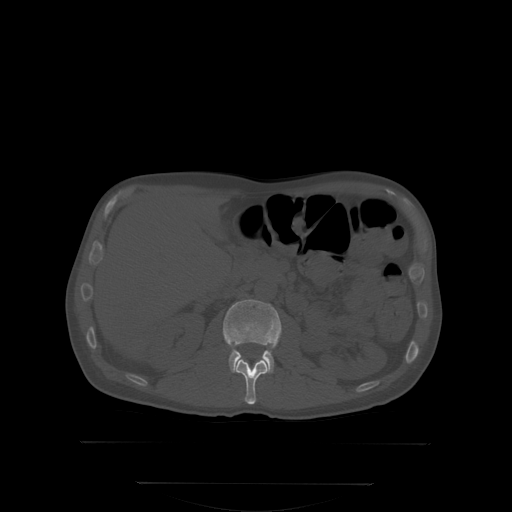
CT including the spine, one axial slice; position 145 of 350 along the scan axis; bone window (W 1800 / L 400 HU); 2.5 mm slice thickness; 512 × 512 image matrix. Male patient, age 58 years. Case-level facts recorded for this patient, not image findings: primary cancer: prostate.
Annotated regions visible in this slice (semi-automatically segmented with operator editing):
- L1 vertebra: bounding box [x1, y1, x2, y2] px = [234, 358, 269, 405]
- L2 vertebra: [223, 299, 281, 371]